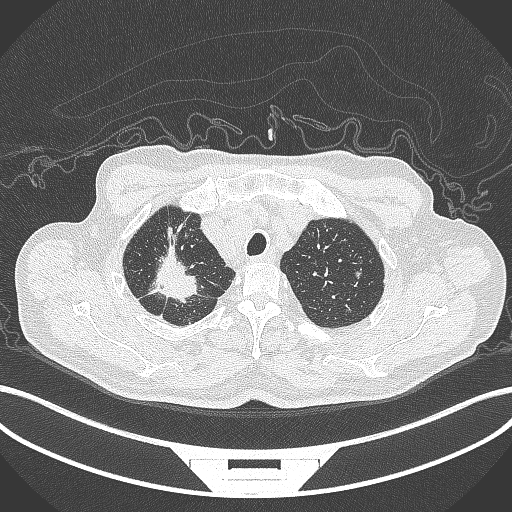
Chest CT, one axial slice; slice 332 of 407 in the series (ordered by position); reconstruction kernel B70f; lung window (W 1500 / L -600 HU); 512 × 512 image matrix. Patient: male, 69 years. Case-level facts recorded for this patient, not image findings: clinical TNM (as recorded): T1c N1 M1.
Annotated regions visible in this slice (bounding box drawn by a radiologist):
- lung tumour (recorded histology: adenocarcinoma): box from (x=149, y=246) to (x=205, y=307) px